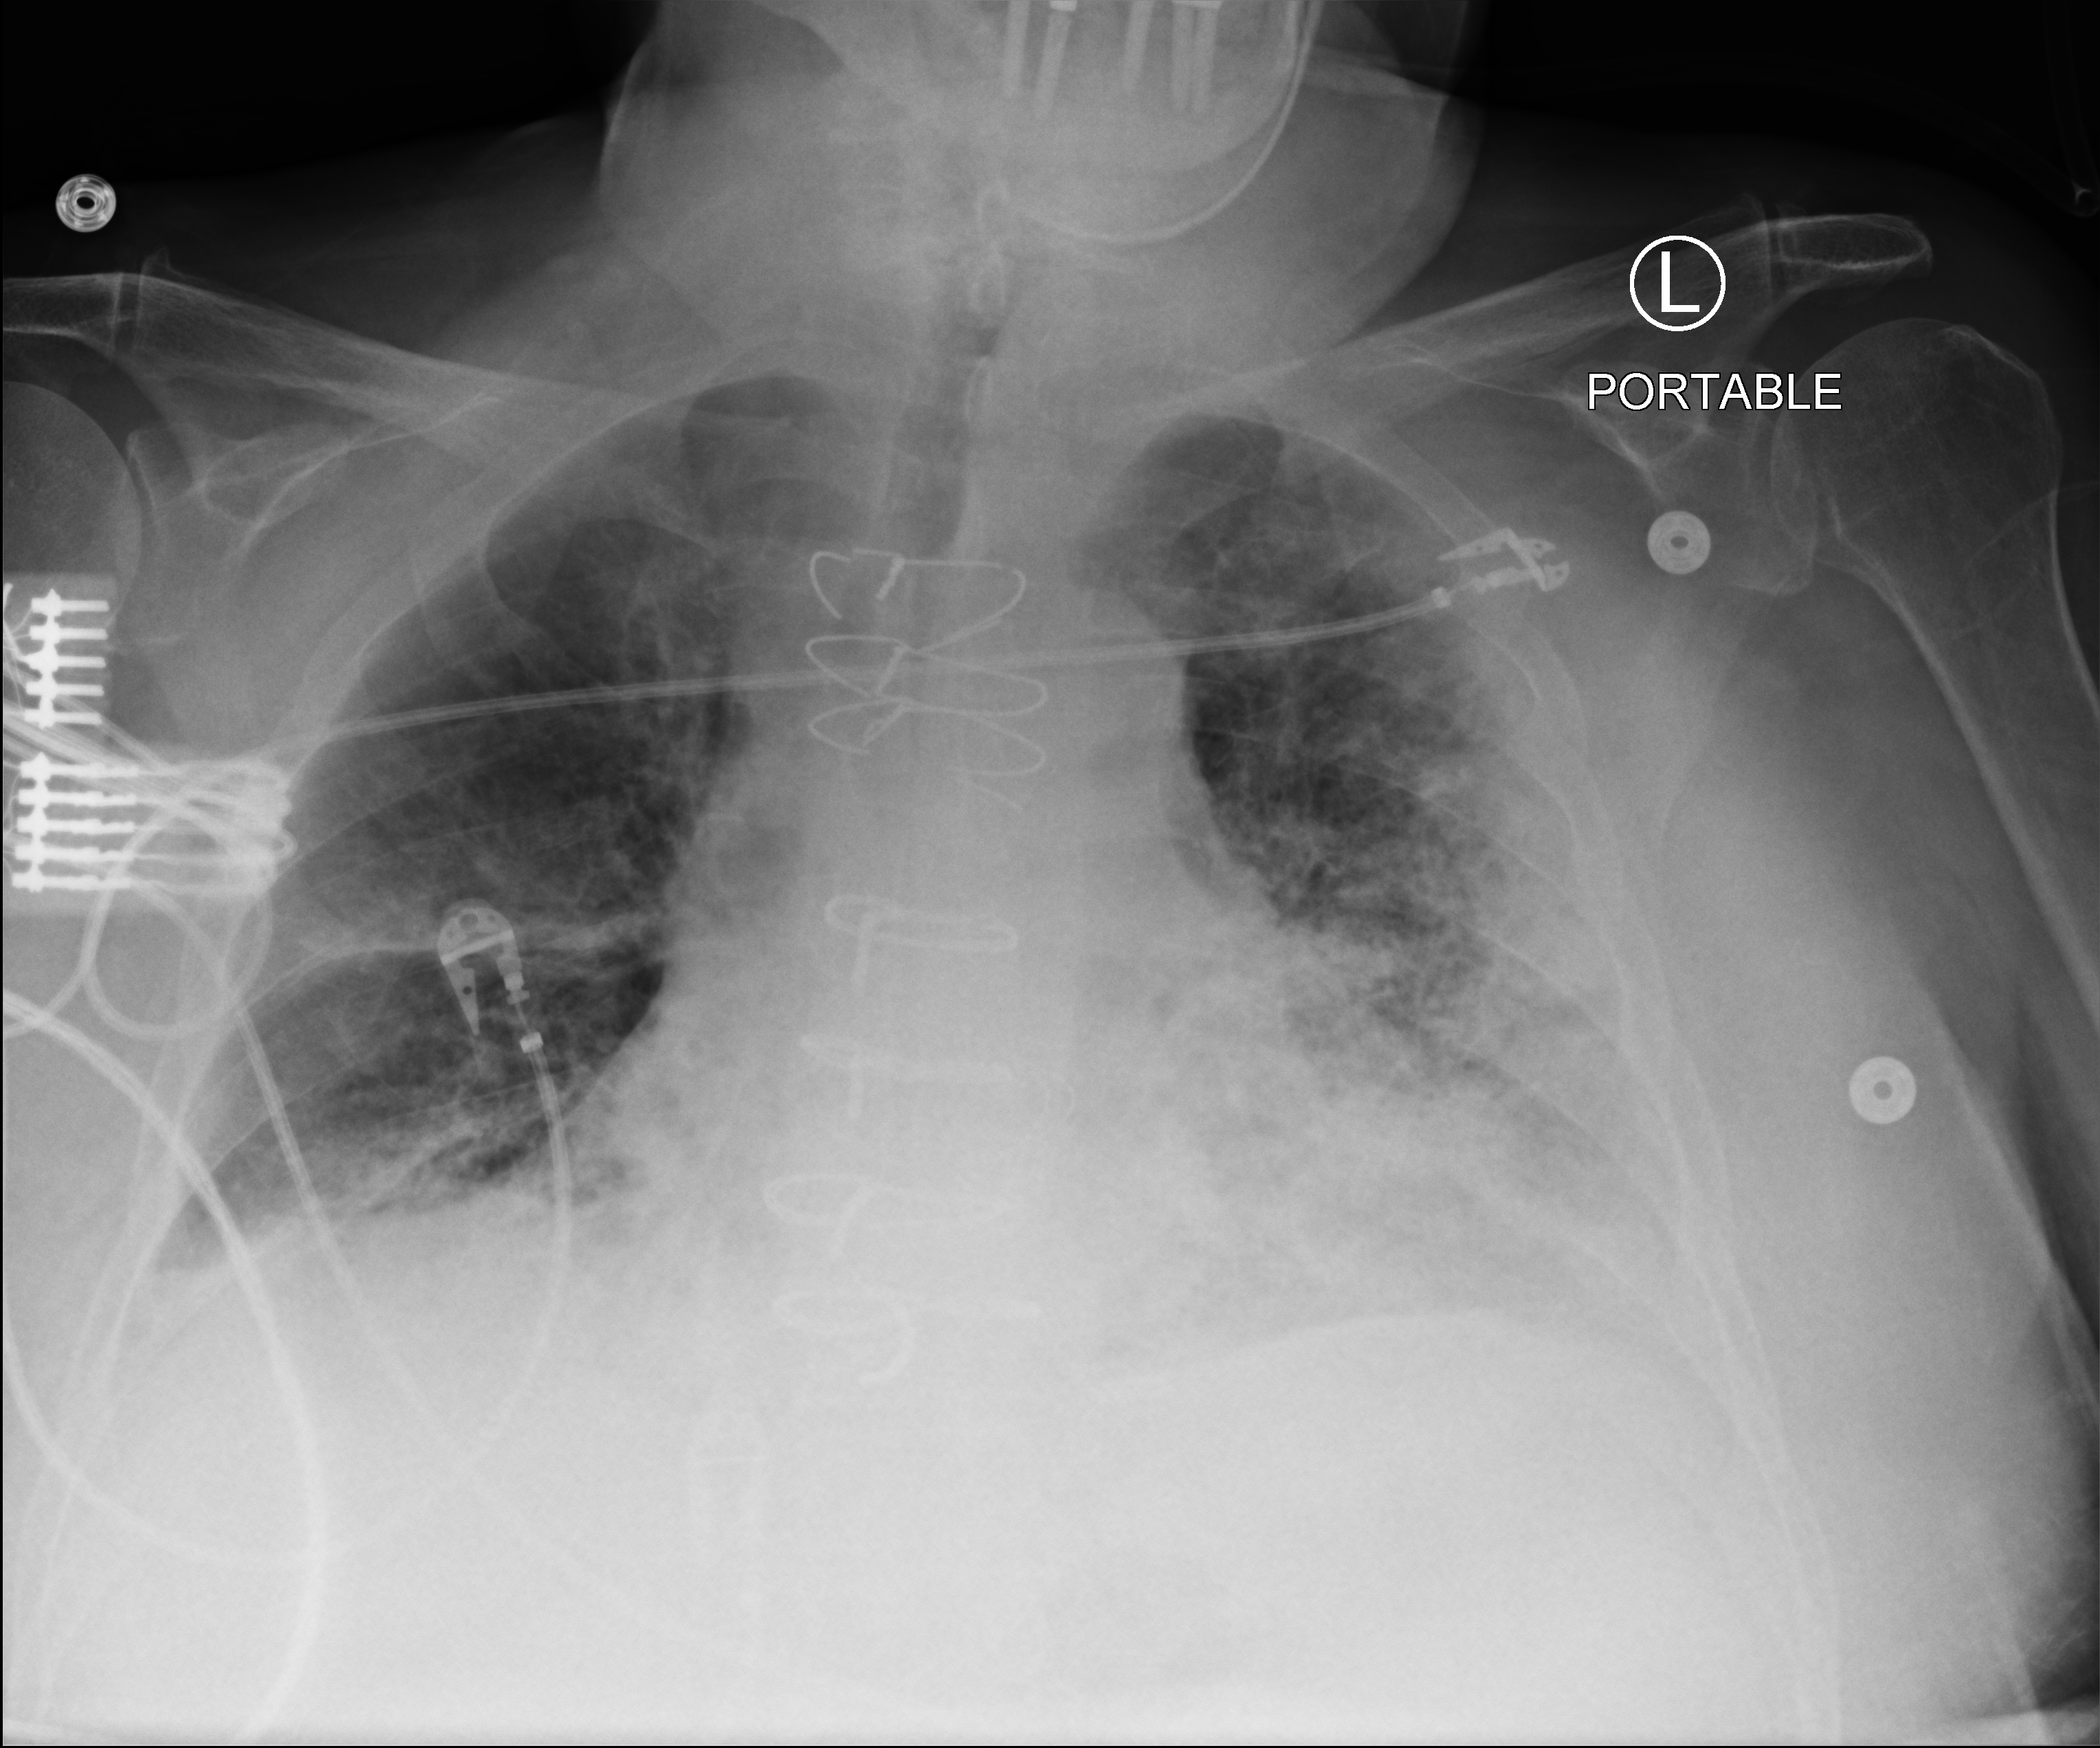
Bedside chest radiograph (computed radiography), anteroposterior (AP) projection. Patient hospitalised with COVID-19; male, aged 75–90 years.
Admission-level facts for this patient (not findings on this image; timing relative to this image not recorded): length of hospital stay: 23 days; mechanically ventilated during this hospital stay: no.